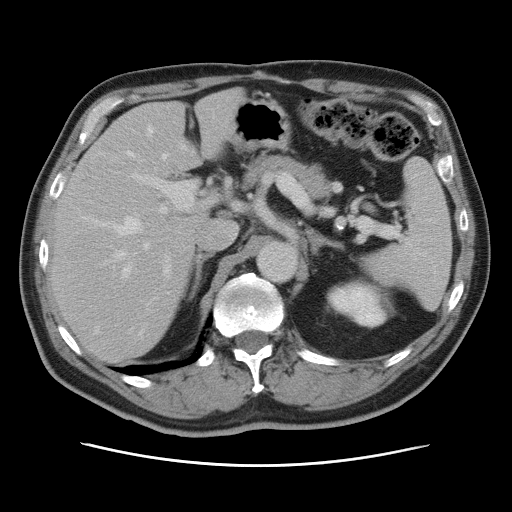
Contrast-enhanced abdominal CT, one axial slice; slice 50 of 80 in the series (ordered by position); 120 kVp; intravenous contrast given; soft-tissue window (W 400 / L 40 HU); 5 mm slice thickness; 512 × 512 image matrix, field of view 370 × 370 mm. Male patient, age 69 years. From the clinical record (not read from this slice): diagnosis: colorectal cancer liver metastases, imaged before liver resection; multiple liver metastases: no; largest metastasis: 5 cm.
Outlined on this slice (expert manual segmentation):
- hepatic veins: bounding box (x1, y1, x2, y2) in pixels: (95, 126, 169, 336)
- liver: (51, 91, 239, 361)
- planned liver remnant (the part of the liver to remain after resection): (50, 91, 239, 362)
- portal vein (with intrahepatic branches): (102, 173, 195, 305)